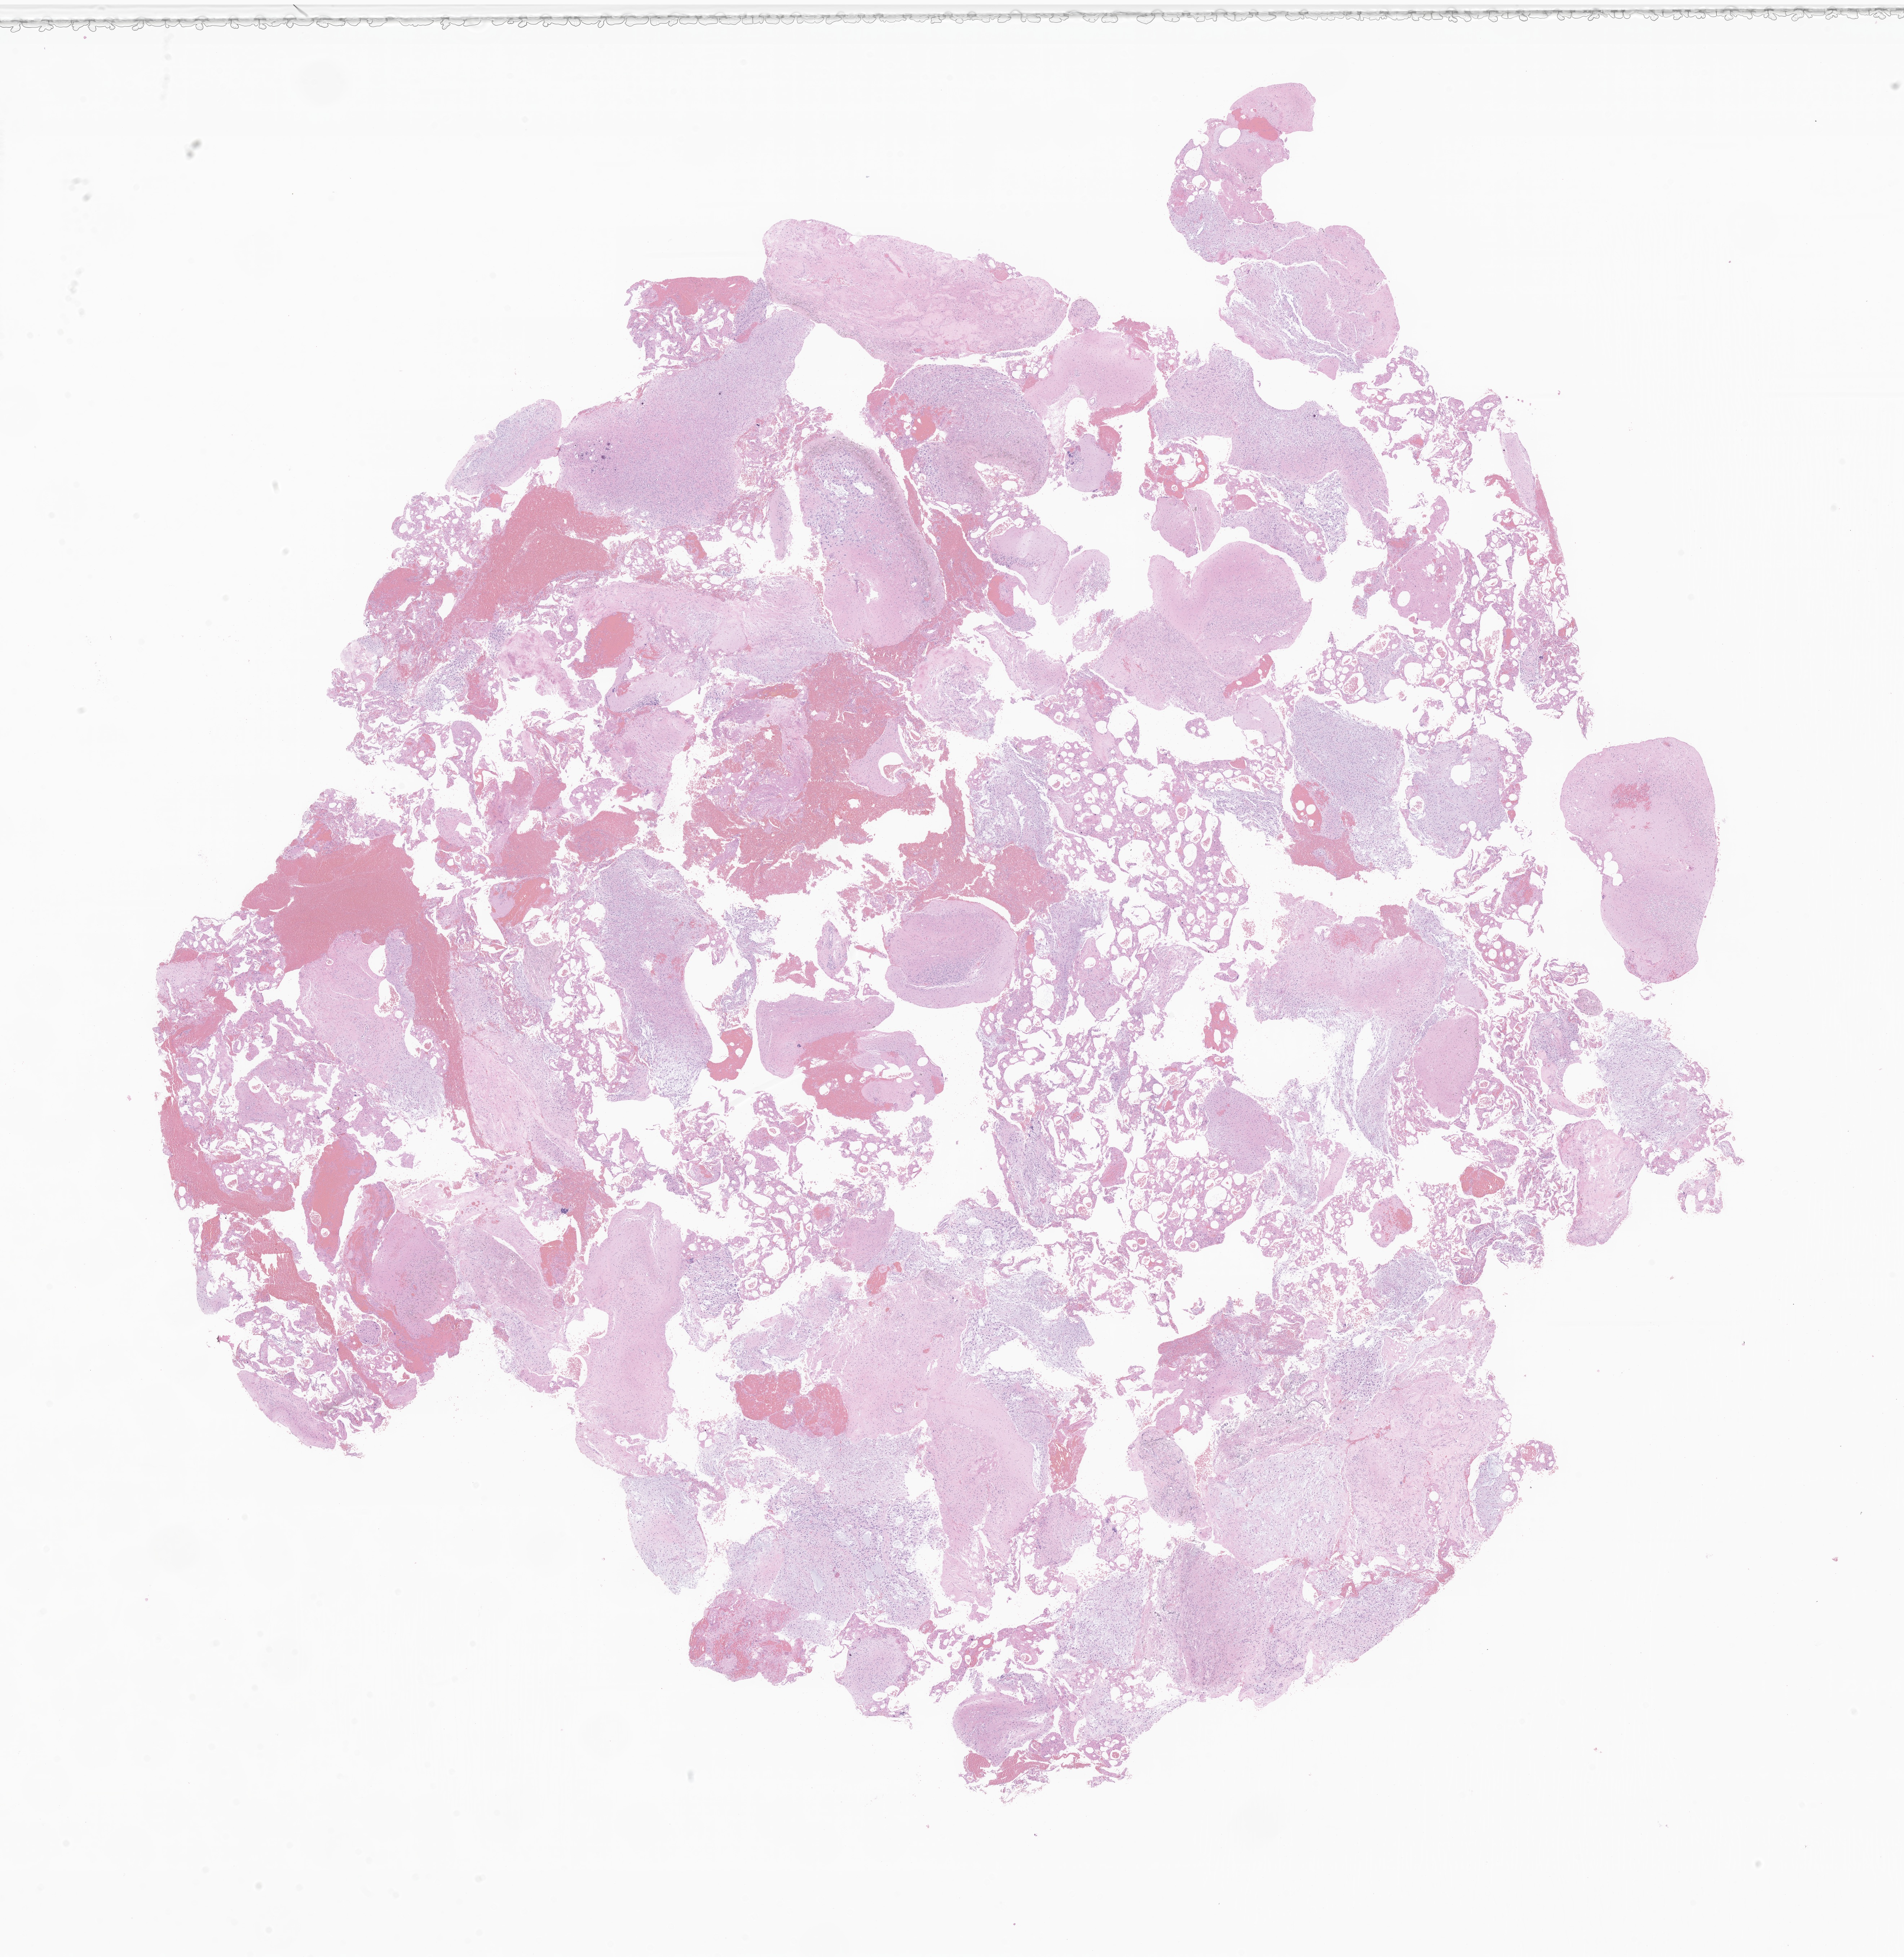
Digitized H&E-stained section of tumor tissue from the brain, a low-resolution overview of the entire scanned area, about 22.3 x 22.9 mm; FFPE section. Female patient, age 186 months (15 years 6 months).
* diagnosis (ICD-O-3 morphology term): Pilocytic astrocytoma